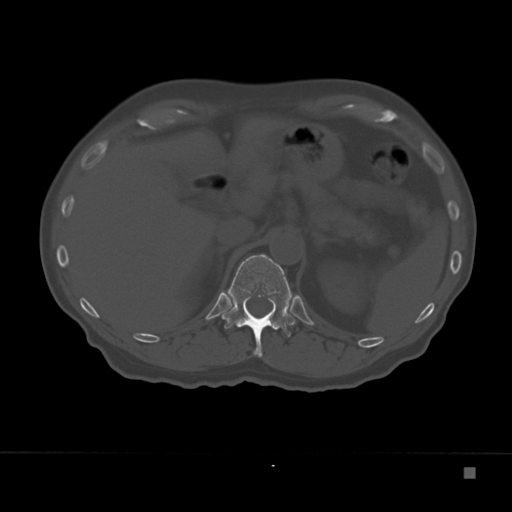
CT including the spine, one axial slice; position 133 of 332 along the scan axis; bone window (W 1800 / L 400 HU); 512 × 512 image matrix, field of view 389 × 389 mm. Patient: male, 72 years. From the clinical record (not read from this slice): primary cancer: skeletal.
Annotated regions visible in this slice (semi-automatically segmented with operator editing):
- T12 vertebra: bounding box [x1, y1, x2, y2] px = [222, 254, 295, 357]